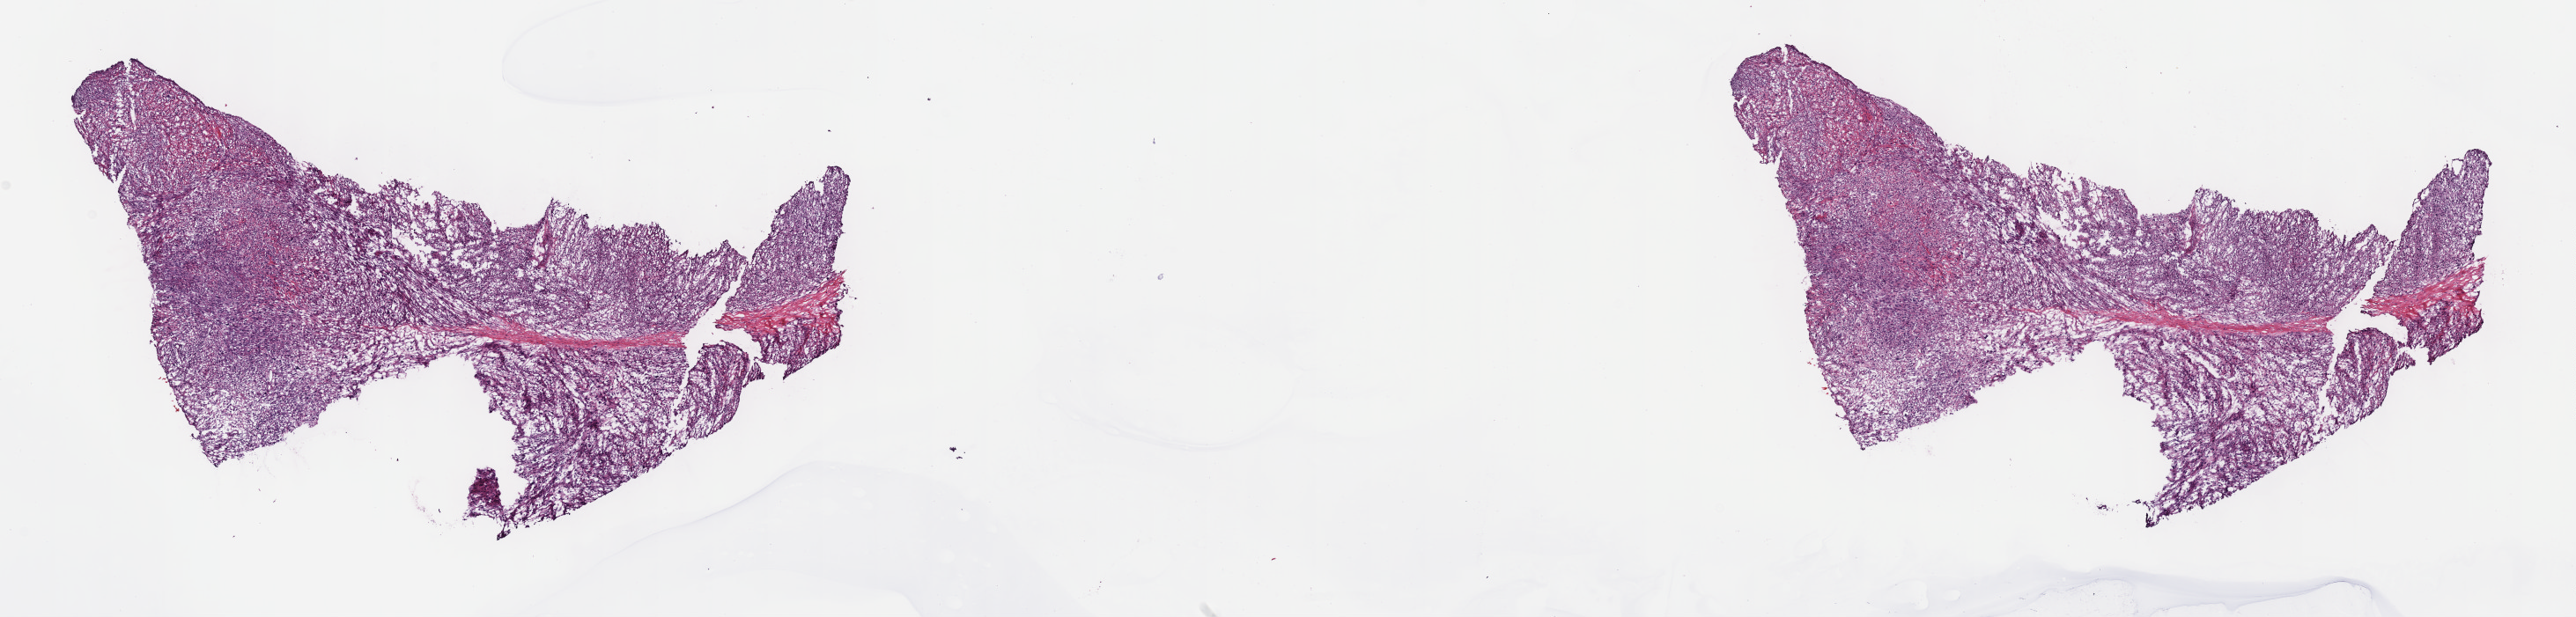
Whole-slide histology image, H&E-stained, shown as a low-resolution overview of the whole scanned area (about 23.7 x 5.7 mm), frozen section from the top of the tissue portion, sample: primary tumour, connective, subcutaneous and other soft tissues. Male, age 66 years at initial diagnosis. Pathologist review of this section (percent, as recorded): tumour cells 80%, tumour nuclei 80%, normal cells 0%, stromal cells 20%, necrosis 0%. Inflammatory infiltration, as recorded: lymphocyte infiltration 2%, monocyte infiltration 1%, neutrophil infiltration 3%.
Diagnosis: Undifferentiated sarcoma (connective, subcutaneous and other soft tissues of pelvis).